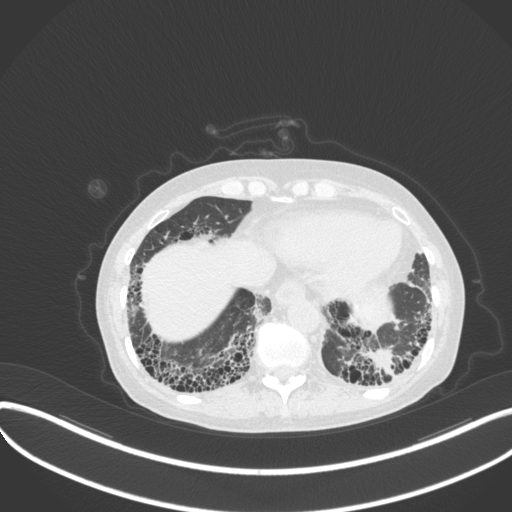
Chest CT, one axial slice; slice 65 of 373 in the series (ordered by position); reconstruction kernel B31f; 120 kVp; lung window (W 1500 / L -600 HU); 1 mm slice thickness; 512 × 512 image matrix. Female patient, age 56 years. From the clinical record (not read from this slice): clinical TNM (as recorded): T1 N0 M0.
Annotated regions visible in this slice (bounding box drawn by a radiologist):
- lung tumour (recorded histology: adenocarcinoma): bounding box <361,343,402,382> (left, top, right, bottom; pixels)